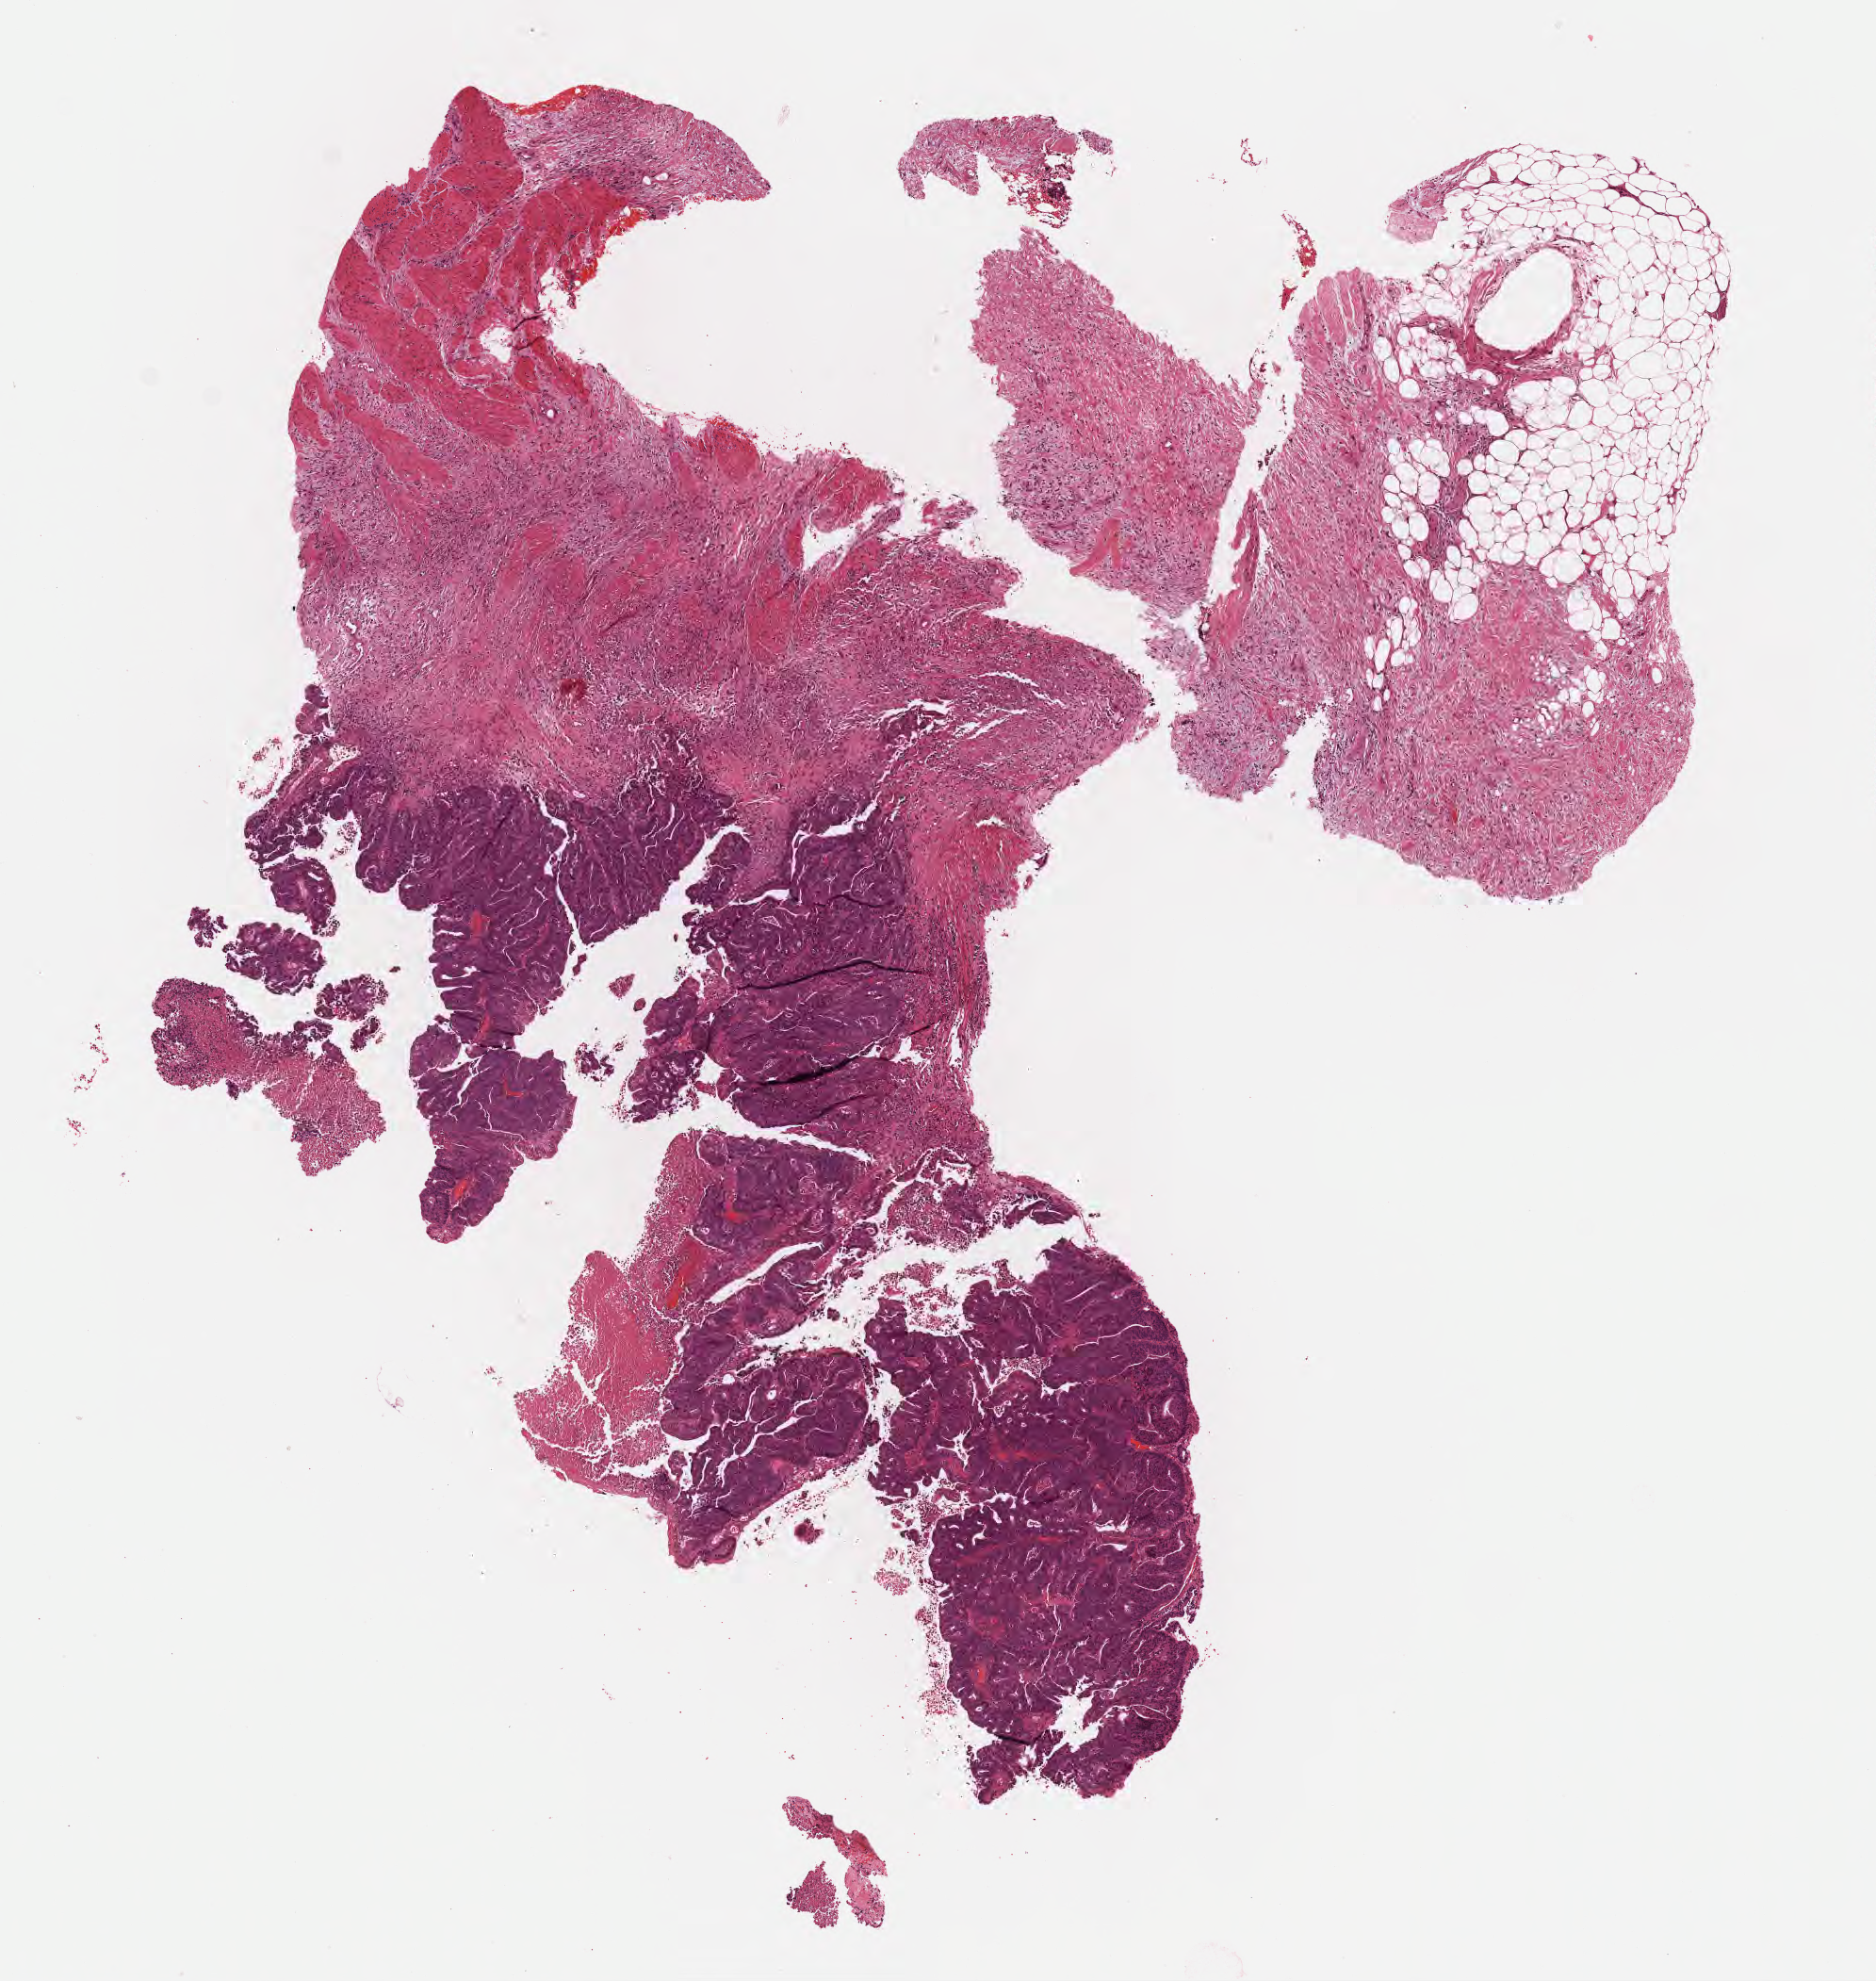
Digitized haematoxylin and eosin-stained section — a low-resolution overview of the entire scanned area, about 8.1 x 8.5 mm; formalin-fixed paraffin-embedded section; primary tumor; site: rectum. Patient: male, age at initial diagnosis 61 years. Tumor grade: G2 (moderately differentiated). Pathologist review of this section (percent, as recorded): tumor cells 80%, tumor nuclei 80%, stromal cells 16%, necrosis 4%, normal cells 0%. Inflammatory infiltration, as recorded: lymphocyte infiltration 4%, monocyte infiltration 1%, neutrophil infiltration 5%.
• histologic diagnosis: Adenocarcinoma, NOS
• AJCC pathologic stage: Stage IIA